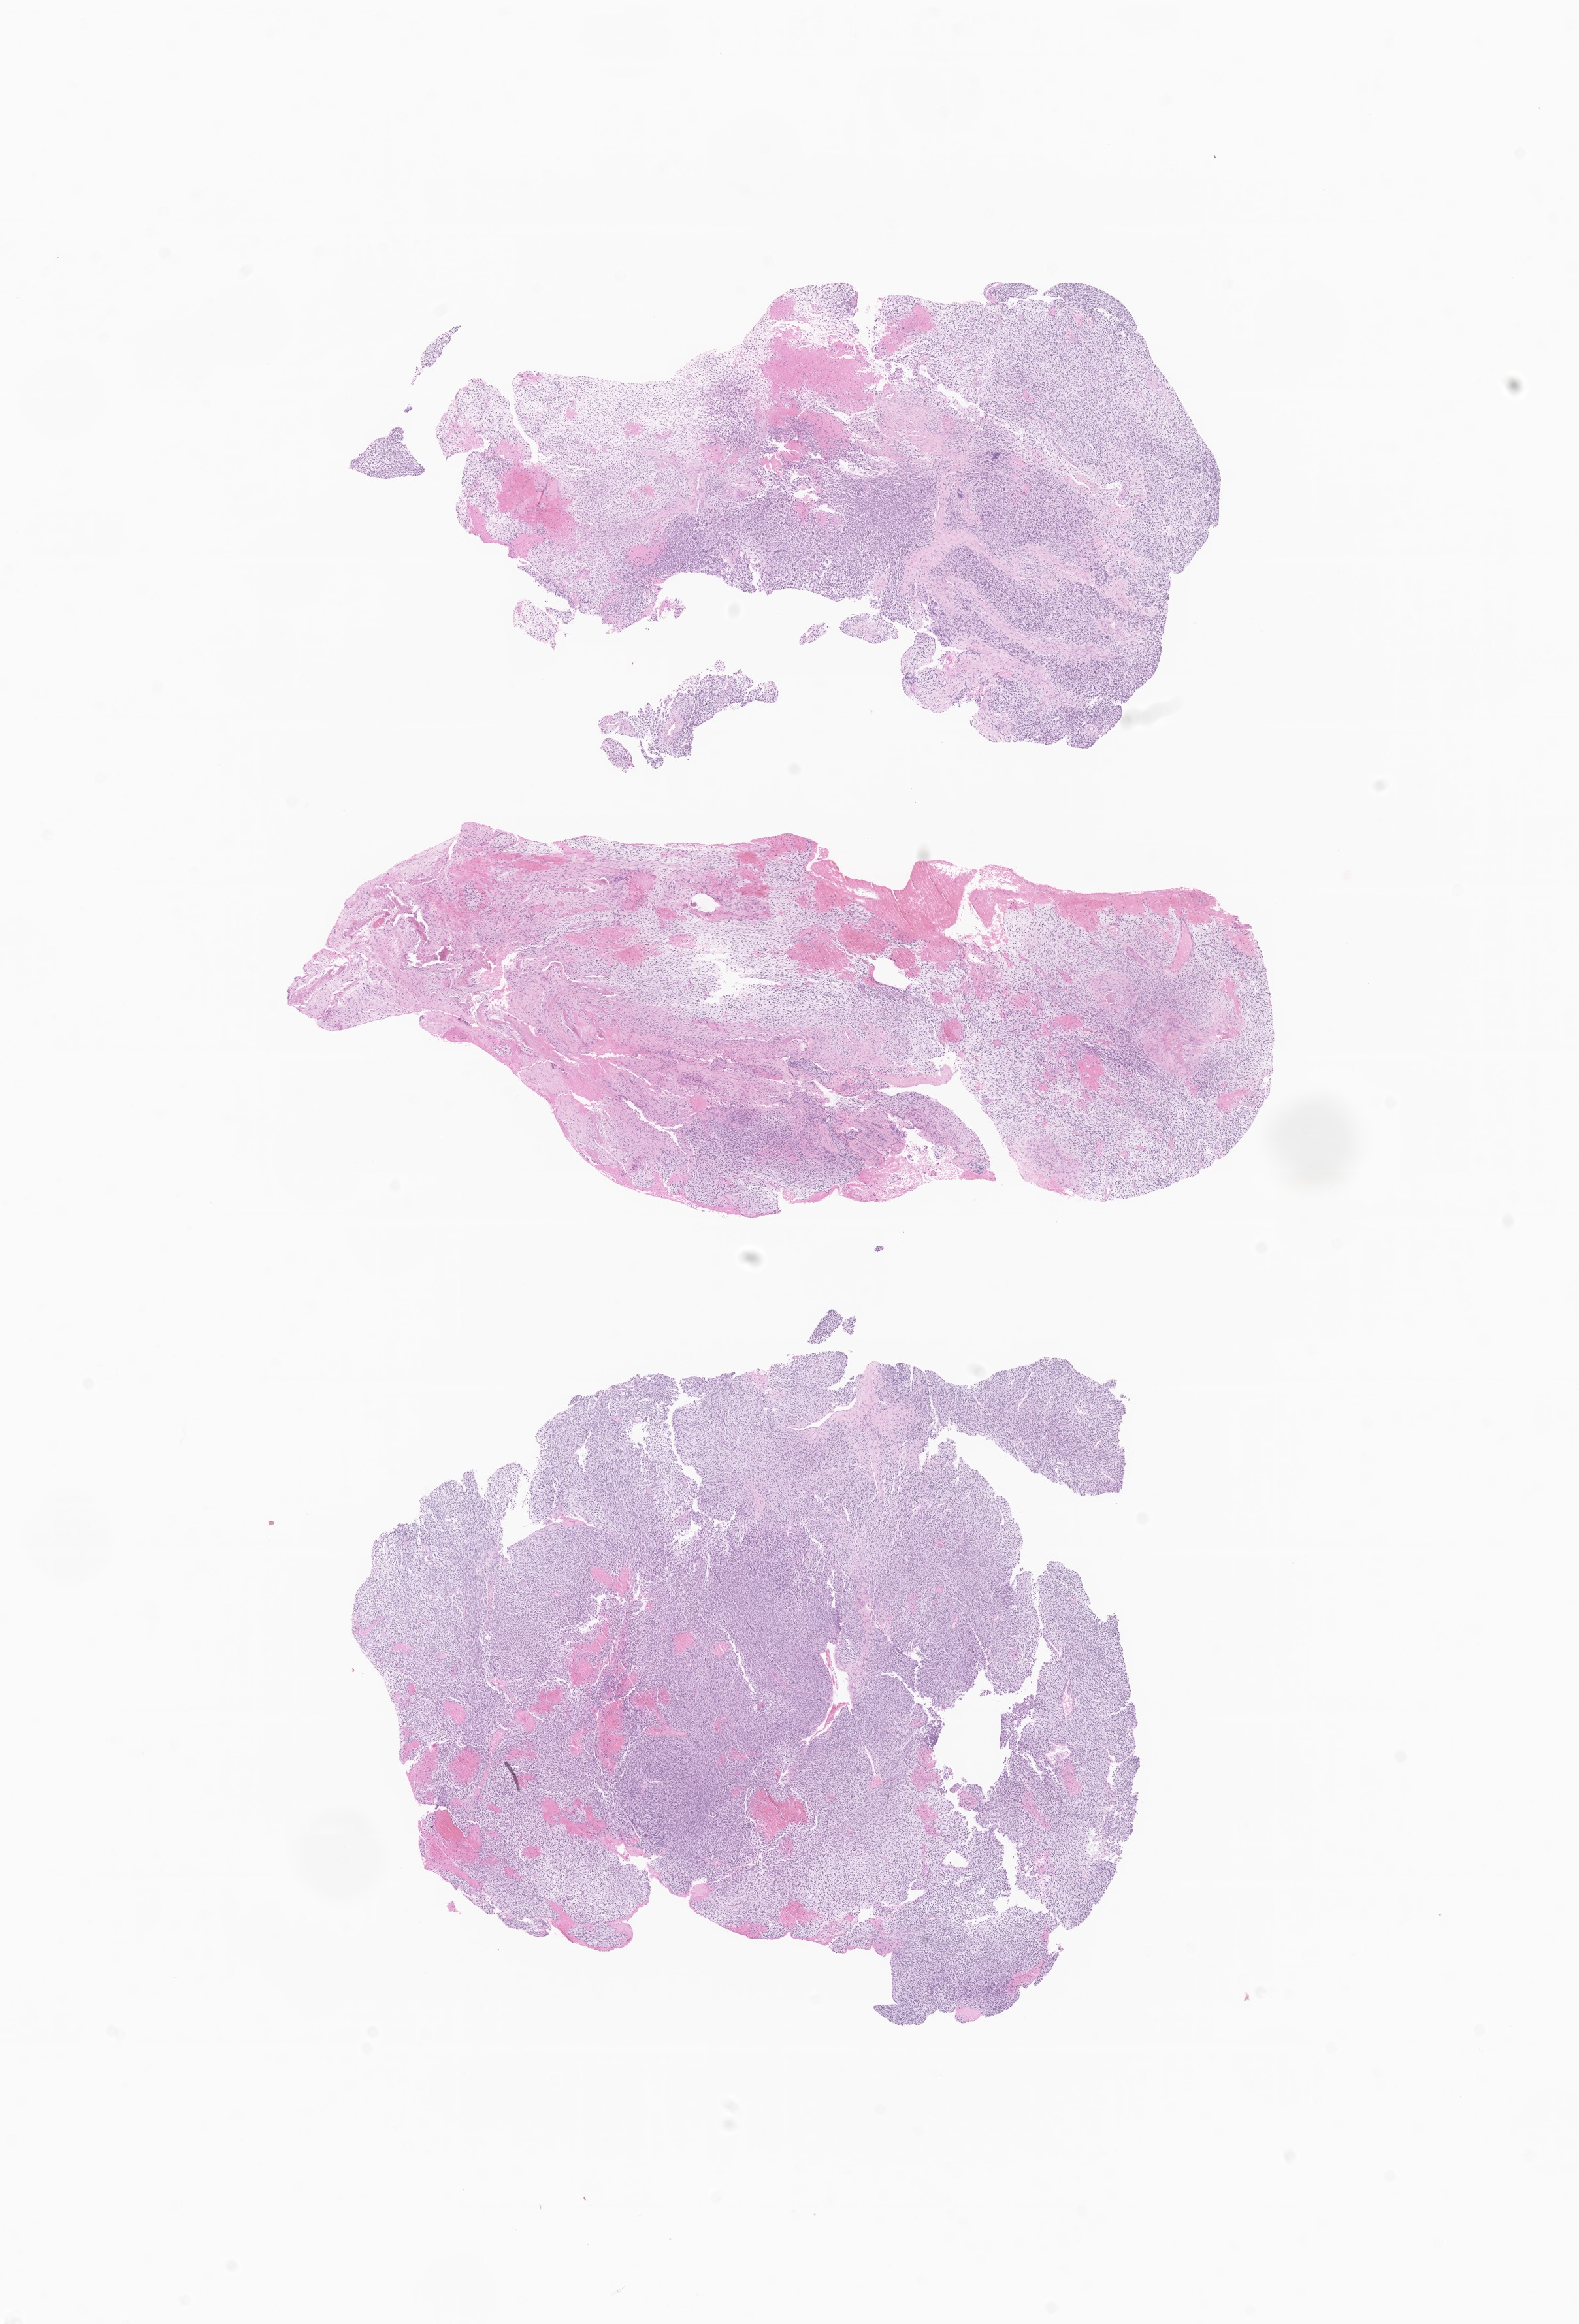
Digitized hematoxylin and eosin (H&E)-stained section of tumor tissue from the nasopharynx, shown as a low-resolution overview of the whole scanned area (about 10.2 x 15.0 mm), FFPE section. Patient: male, age 58 months.
Recorded diagnosis: Rhabdomyosarcoma, NOS.